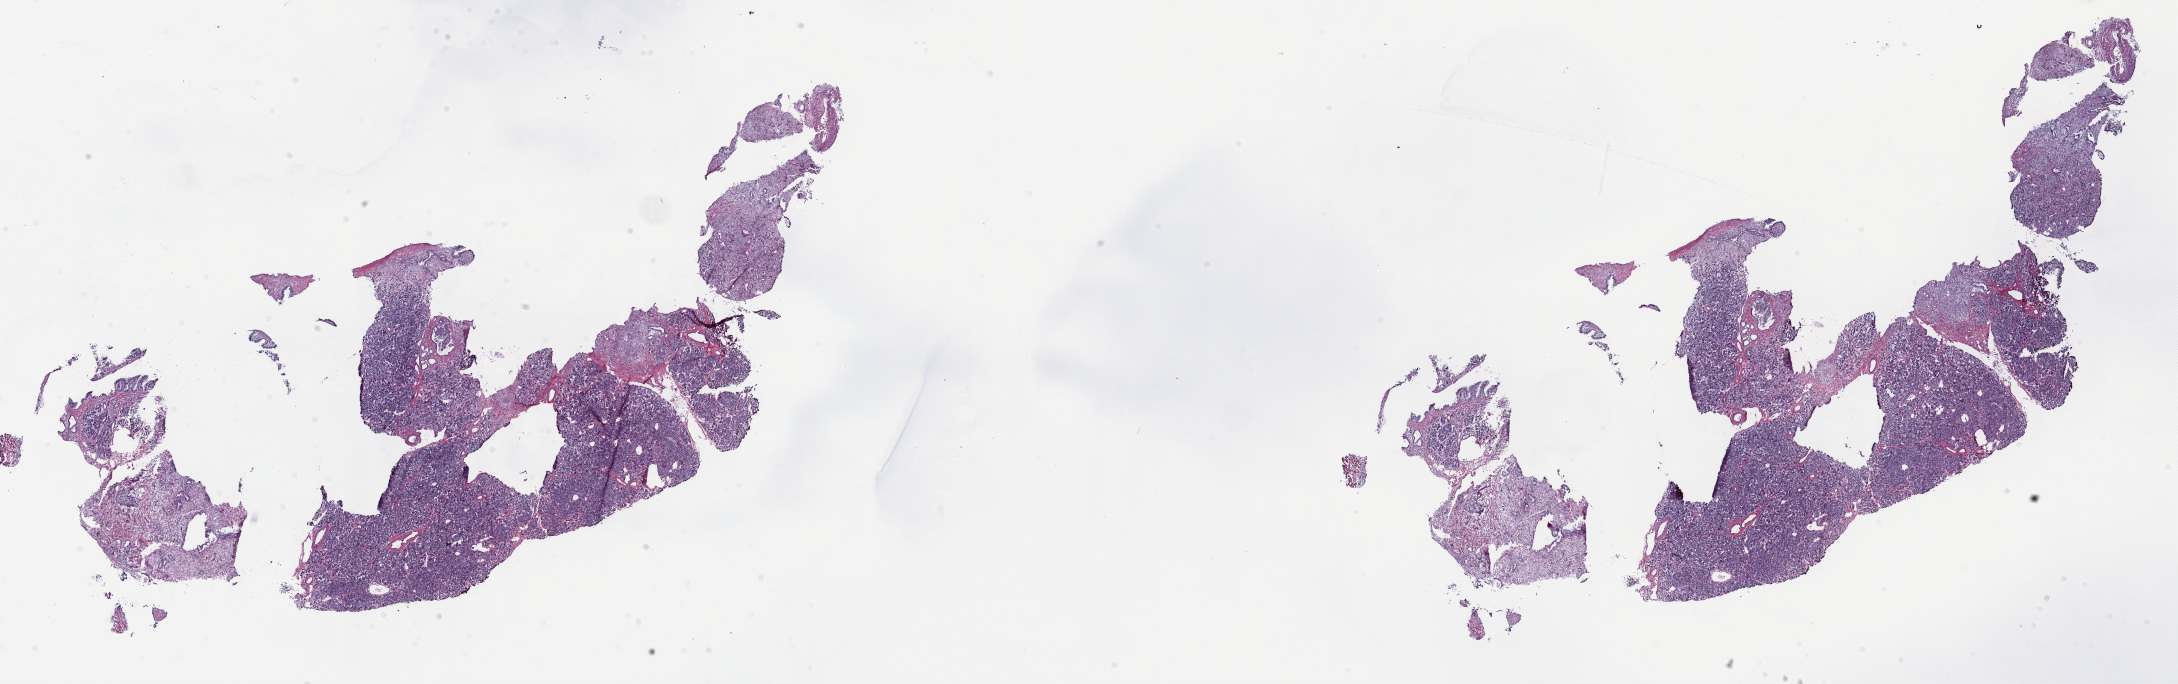
Hematoxylin and eosin (H&E) stained whole-slide image, whole scanned area (about 35.2 x 11.1 mm, from a 40x scan) shown as a low-resolution overview. Frozen section from the top of the tissue portion. Primary tumour sample from the pancreas. Patient: male, age at initial diagnosis 76 years. Histologic grade: G3 (poorly differentiated). Composition of this section per pathologist review: tumour cells 15%, tumour nuclei 15%, normal cells 60%, stromal cells 25%, necrosis 0%. Inflammatory infiltration, as recorded: lymphocyte infiltration 3%, monocyte infiltration 1%, neutrophil infiltration 4%.
• lymph nodes positive (case pathology): 1 of 1 examined
• histologic diagnosis: Infiltrating duct carcinoma, NOS
• TNM: T2 N1 M0
• AJCC pathologic stage: IIB (7th edition)